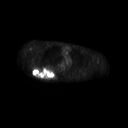
FDG PET of an extremity soft-tissue mass (from a PET/CT study), one axial slice; slice 188 of 267 in the series (ordered by position); 3.27 mm slice thickness; 128 × 128 image matrix, field of view 700 × 700 mm. Male patient, age 61 years. Case-level facts recorded for this patient, not image findings: histological type: pleiomorphic spindle cell undifferentiated; grade: high; site of the primary tumour: right parascapusular.
Structures marked on this image (expert contour drawn on MRI and transferred to this co-registered scan by the dataset authors):
- gross tumour volume including surrounding oedema: box from (x=32, y=66) to (x=58, y=79) px
- gross tumour volume (mass): (x=32, y=66)–(x=55, y=78)